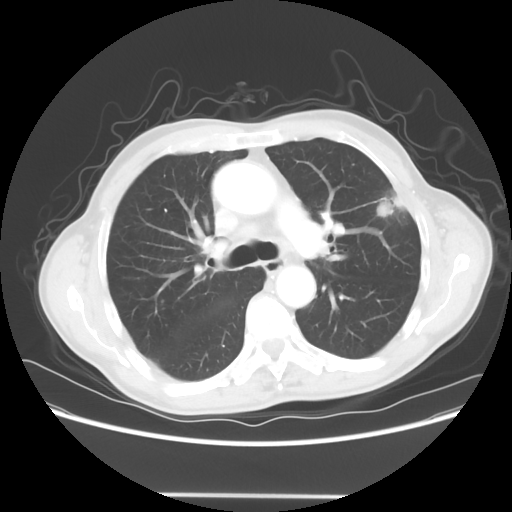
Chest CT, one axial slice; position 40 of 64 along the scan axis; 120 kVp; lung window (W 1500 / L -600 HU); 512 × 512 image matrix, field of view 392 × 392 mm. Patient: male, 71 years. From the clinical record (not read from this slice): clinical TNM (as recorded): T1c N0 M0; histopathological grade: G2-3.
Structures marked on this image (bounding box drawn by a radiologist):
- lung tumour (recorded histology: adenocarcinoma): bounding box [x1, y1, x2, y2] px = [366, 186, 416, 233]